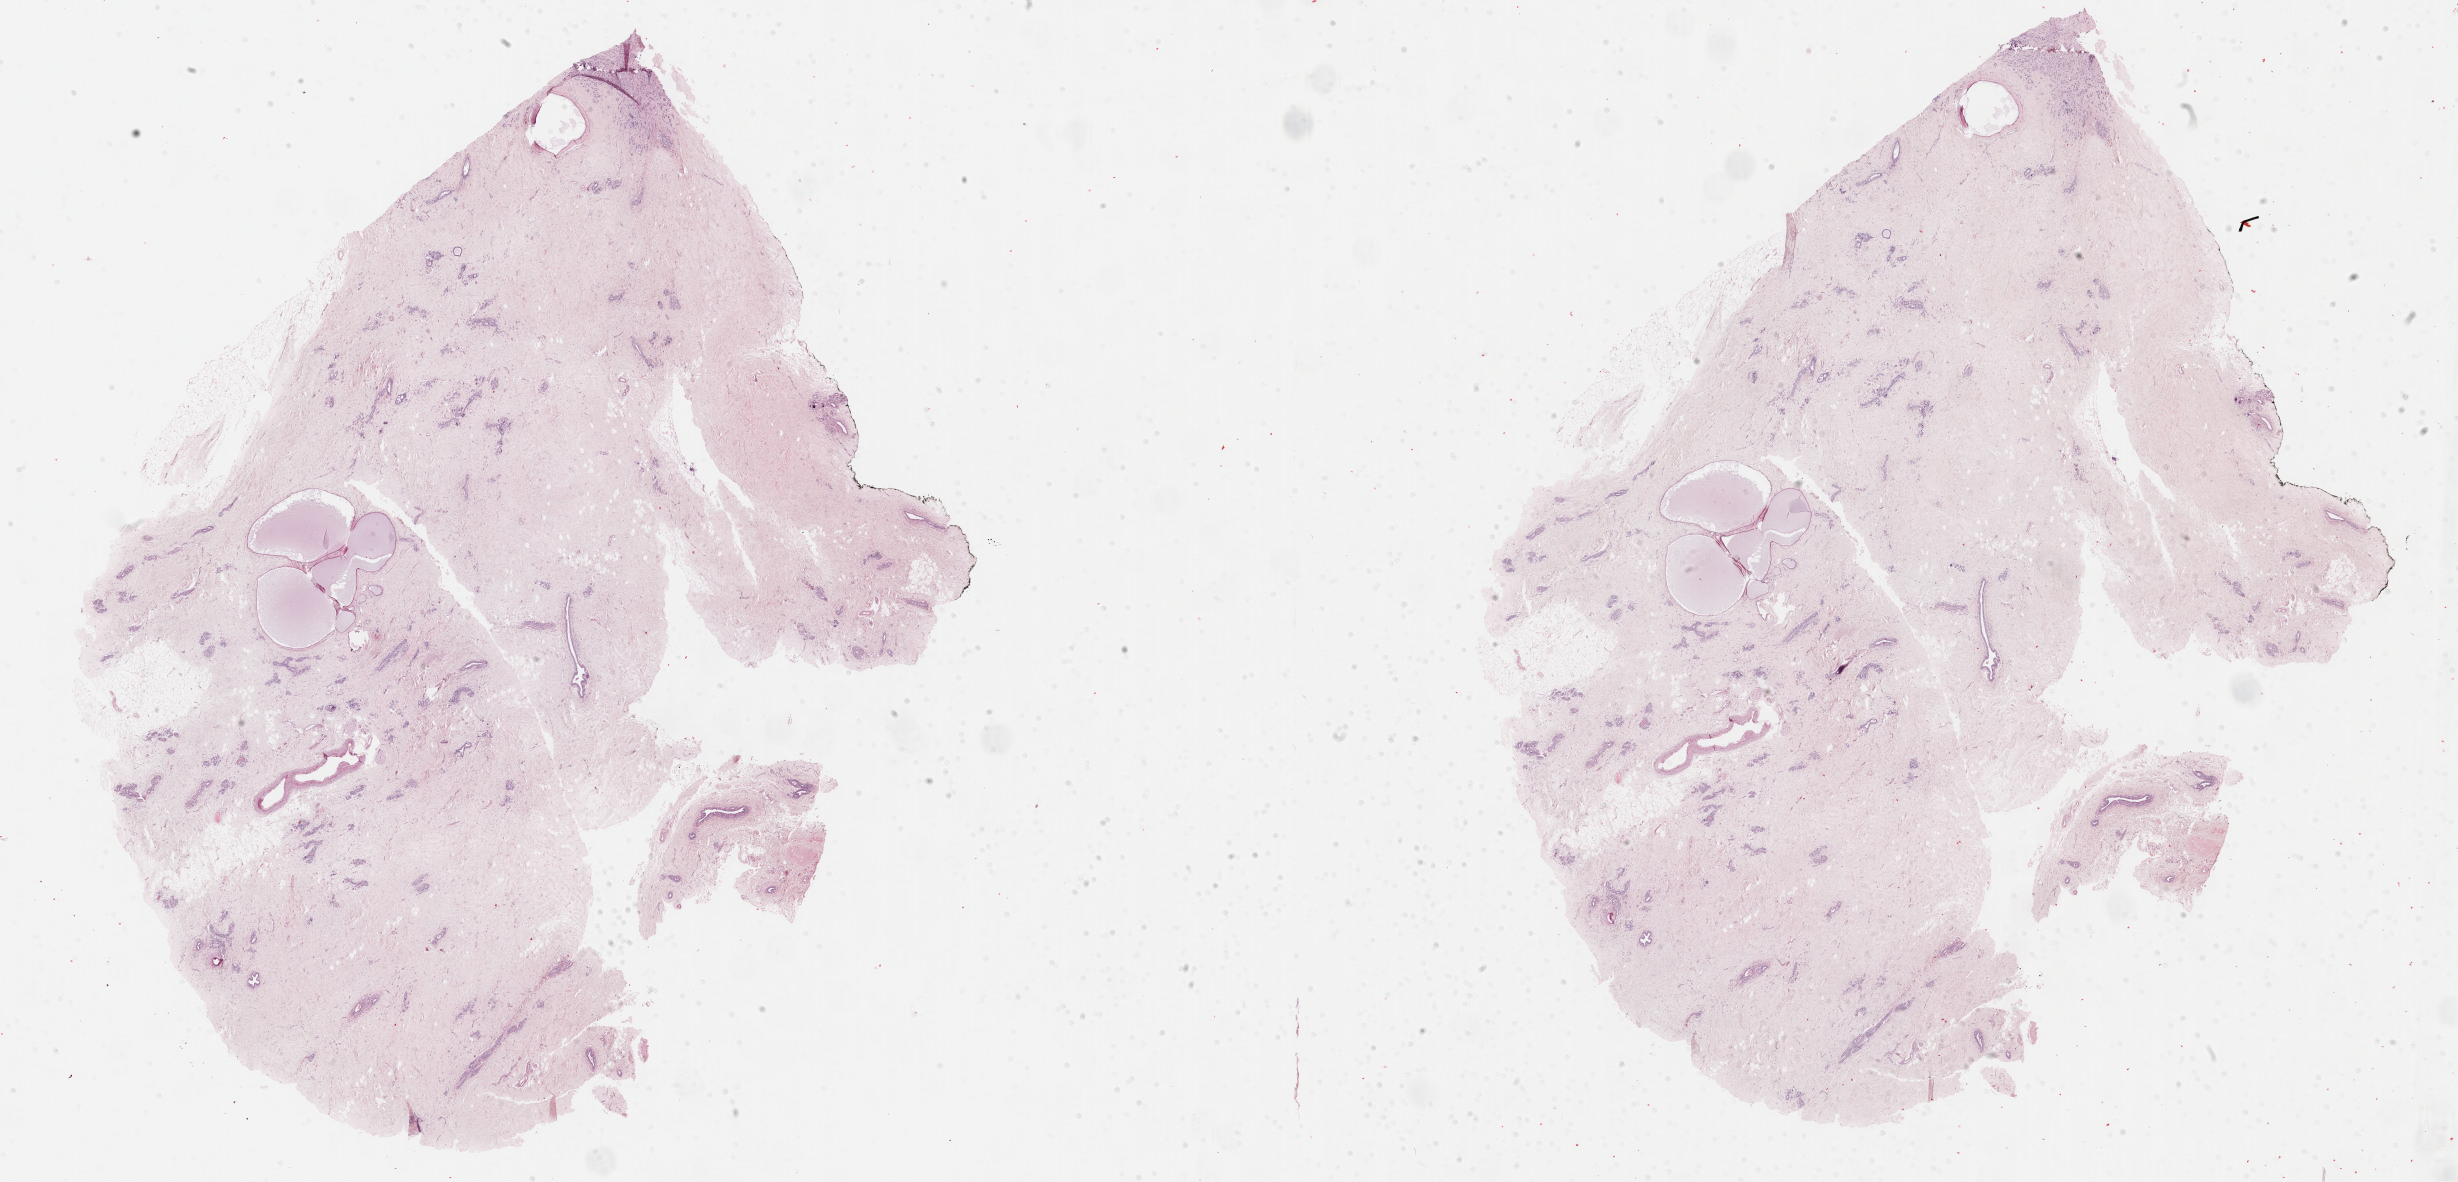
Hematoxylin and eosin (H&E) stained whole-slide image, whole scanned area (about 39.8 x 19.1 mm, slide scanned at 40x) shown as a low-resolution overview; FFPE section; sample: primary tumour, breast. Female, age 53 years at initial diagnosis.
- laterality: left
- TNM: T2 N0 M0
- AJCC pathologic stage: IIA (7th edition)
- histologic diagnosis: Tubular adenocarcinoma